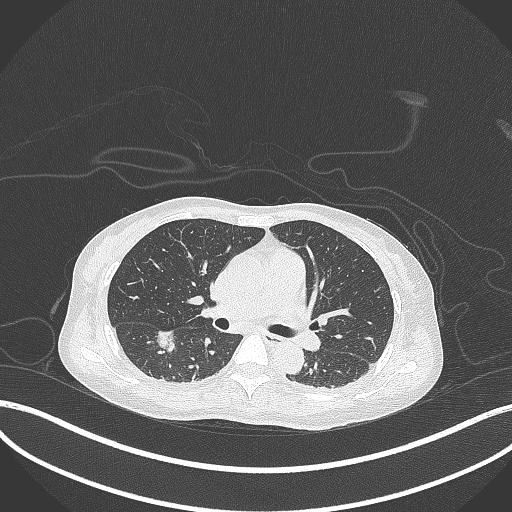
Chest CT, one axial slice. Position 179 of 261 along the scan axis. 120 kVp. Lung window (W 1500 / L -600 HU). 1 mm slice thickness. 512 × 512 image matrix, field of view 400 × 400 mm. Female patient, age 44 years. From the clinical record (not read from this slice): clinical TNM (as recorded): T1c N0 M0.
Structures marked on this image (rectangle marked by the reading radiologist):
- lung tumour (recorded histology: adenocarcinoma): bounding box [x1, y1, x2, y2] px = [156, 325, 182, 355]